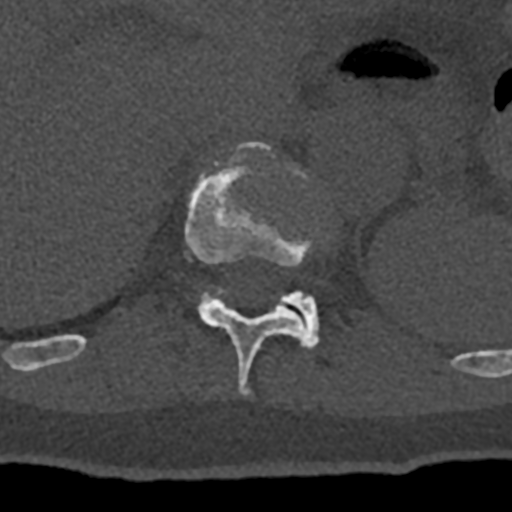
CT including the spine, one axial slice; reconstruction kernel Br40s/3; 120 kVp; bone window (W 1800 / L 400 HU); 0.5 mm slice thickness; 512 × 512 image matrix, field of view 160 × 160 mm. Patient: male, 74 years. Case-level facts recorded for this patient, not image findings: primary cancer: renal; vertebrae with lytic lesions (as recorded): T10, L1, L2, L3, L4, L5.
Outlined on this slice (semi-automatically segmented with operator editing):
- T11 vertebra: bounding box <70,141,311,396> (left, top, right, bottom; pixels)
- T12 vertebra: <200,289,319,350>